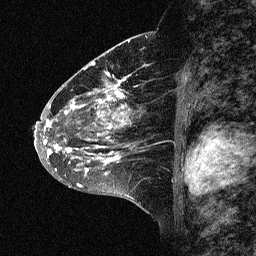
Breast MRI (dynamic contrast-enhanced), one sagittal slice; position 33 of 64 along the scan axis; dynamic contrast-enhanced study with each time point stored as its own series, time point 2 of 3 at this slice position (early post-contrast, ordered by acquisition time); 1.5 T; TE 4.5 ms, TR 11 ms; 2.06 mm slice thickness; 256 × 256 image matrix. Patient: female, 46 years. Case-level facts recorded for this patient, not image findings: setting: breast cancer imaged before/during neoadjuvant chemotherapy; receptor status: HER2-positive.
Structures marked on this image (semi-automatically segmented with operator editing):
- analysis volume of interest (the breast-tissue region the enhancement analysis was run in; not a lesion): bounding box (x1, y1, x2, y2) in pixels: (43, 72, 167, 177)
- tumour enhancement mask (voxels above the 90 % enhancement threshold inside the analysis volume of interest): (43, 72, 148, 174)